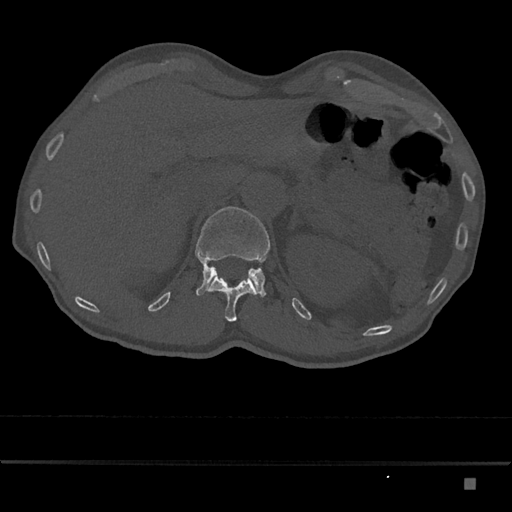
CT including the spine, one axial slice; position 580 of 797 along the scan axis; bone window (W 1800 / L 400 HU); 512 × 512 image matrix. Male patient, age 72 years. Case-level facts recorded for this patient, not image findings: primary cancer: prostate.
Outlined on this slice (semi-automatic segmentation, software-assisted and operator-edited):
- L1 vertebra: bounding box (x1, y1, x2, y2) in pixels: (195, 206, 270, 297)
- T12 vertebra: (204, 275, 256, 322)